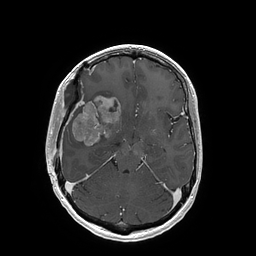
Brain MRI from a brain-tumour surgery series, one axial slice; position 105 of 202 along the scan axis; T1-weighted post-contrast; 1 mm slice thickness; 256 × 256 image matrix, field of view 250 × 250 mm. From the clinical record (not read from this slice): histopathology: Glioblastoma; WHO grade: 4; IDH mutation: no.
Outlined on this slice (outlined manually by an expert reader):
- tumour: bounding box (x1, y1, x2, y2) in pixels: (72, 96, 121, 146)